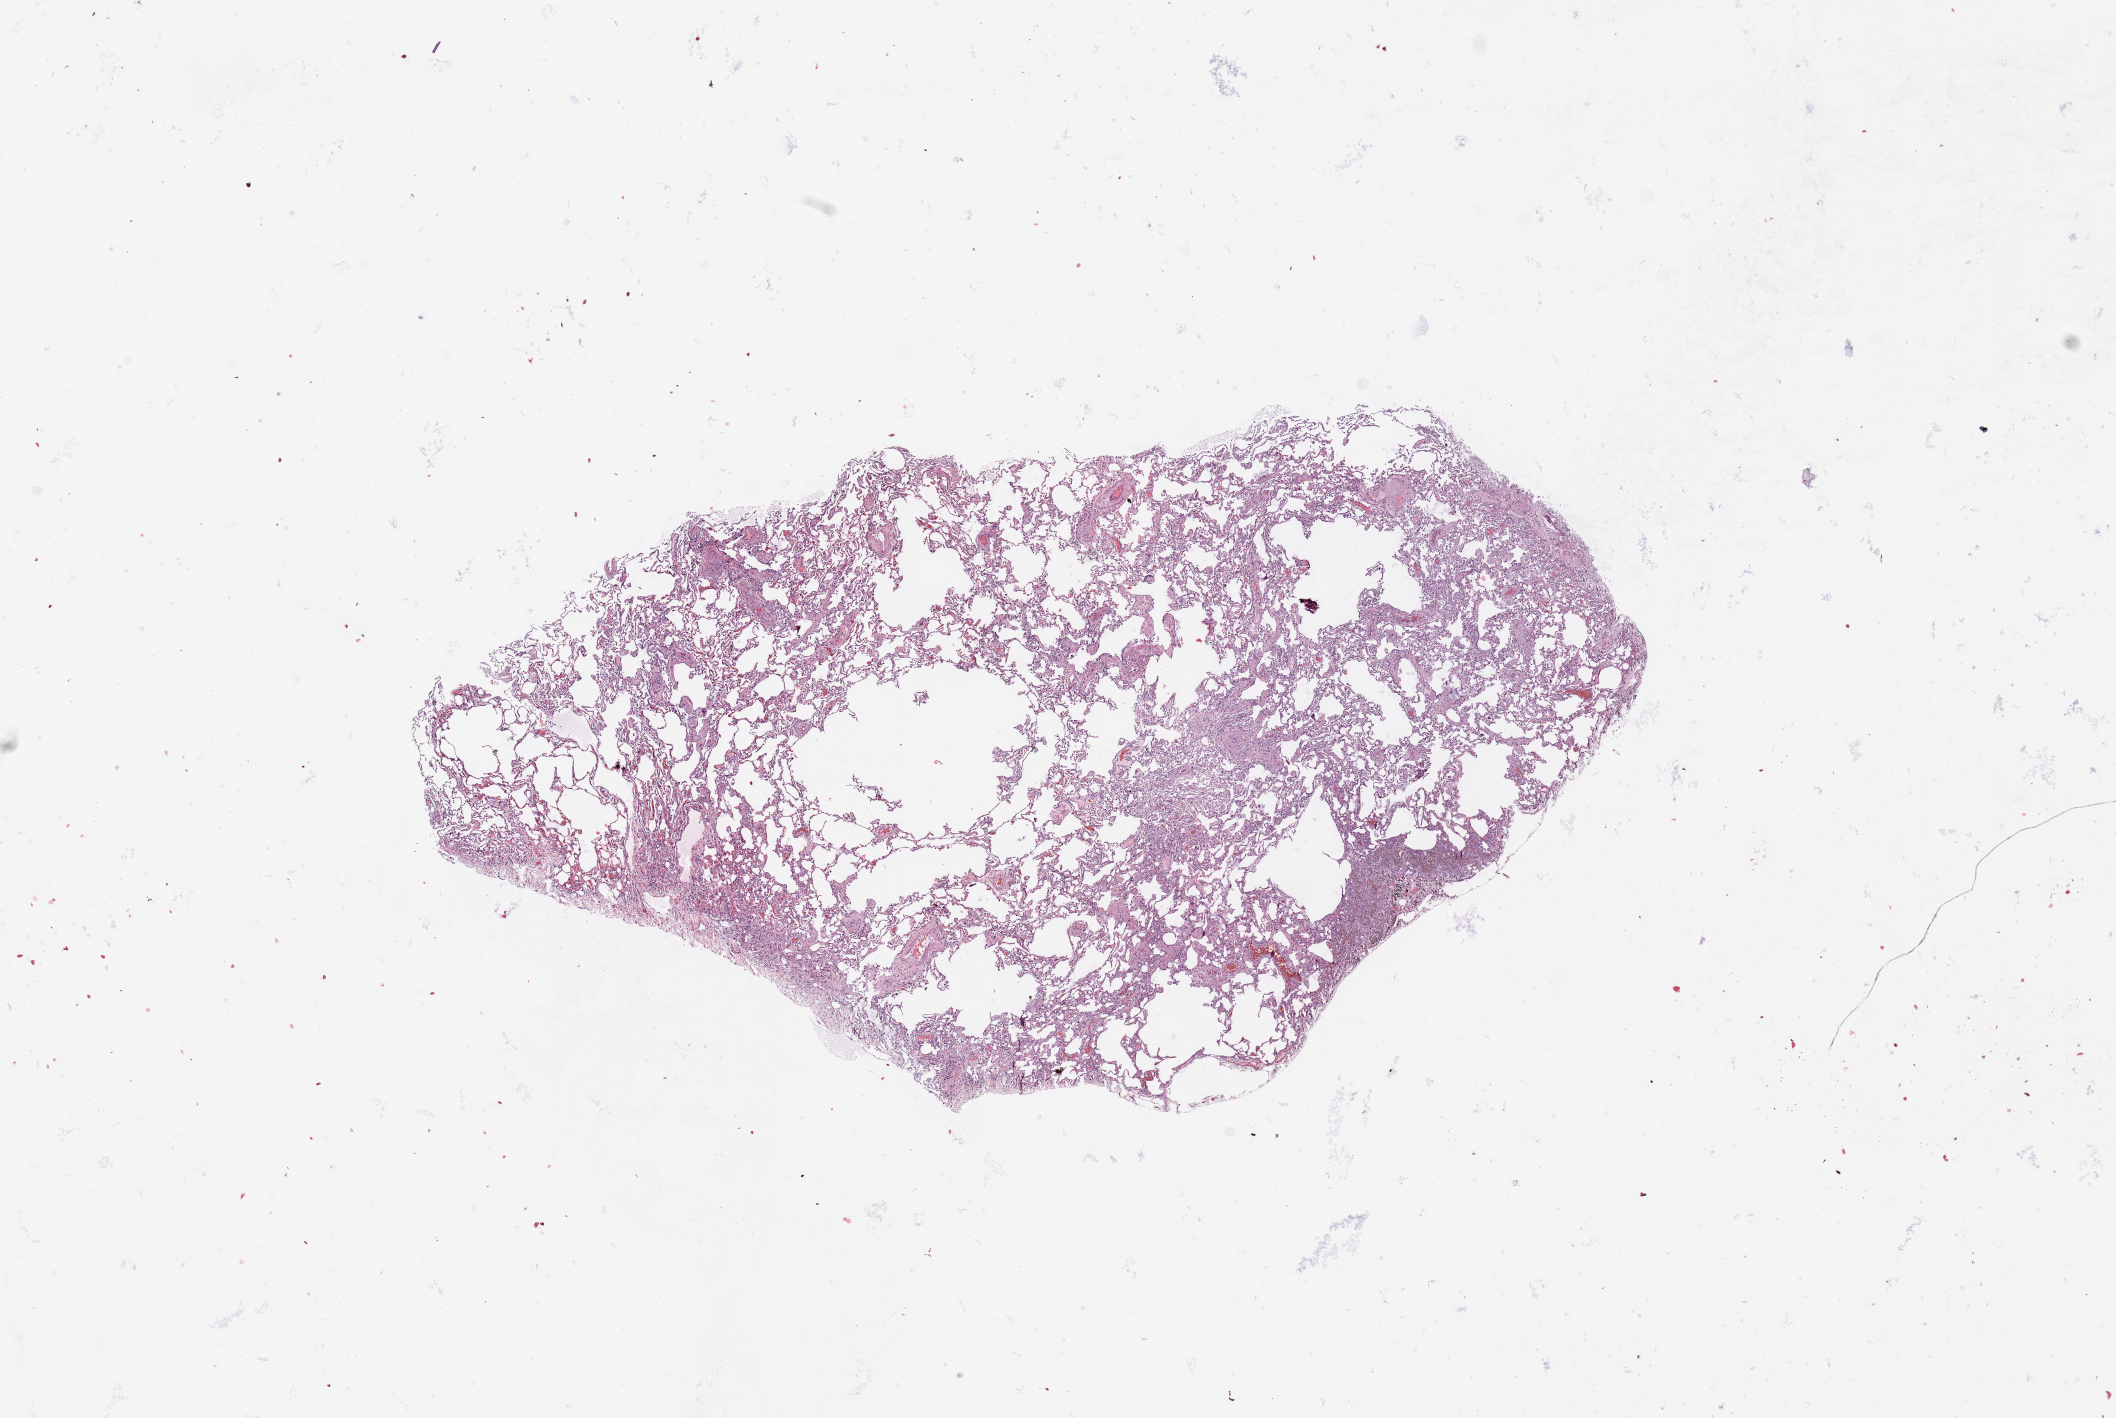
Digitized H&E-stained tissue section (whole slide) — whole scanned area (about 16.7 x 11.2 mm) shown as a low-resolution overview. Lung, normal (non-tumour) tissue. Female, 48 y/o.
- this section: normal (non-tumour) tissue from the same patient
- patient diagnosis: Squamous cell carcinoma, NOS